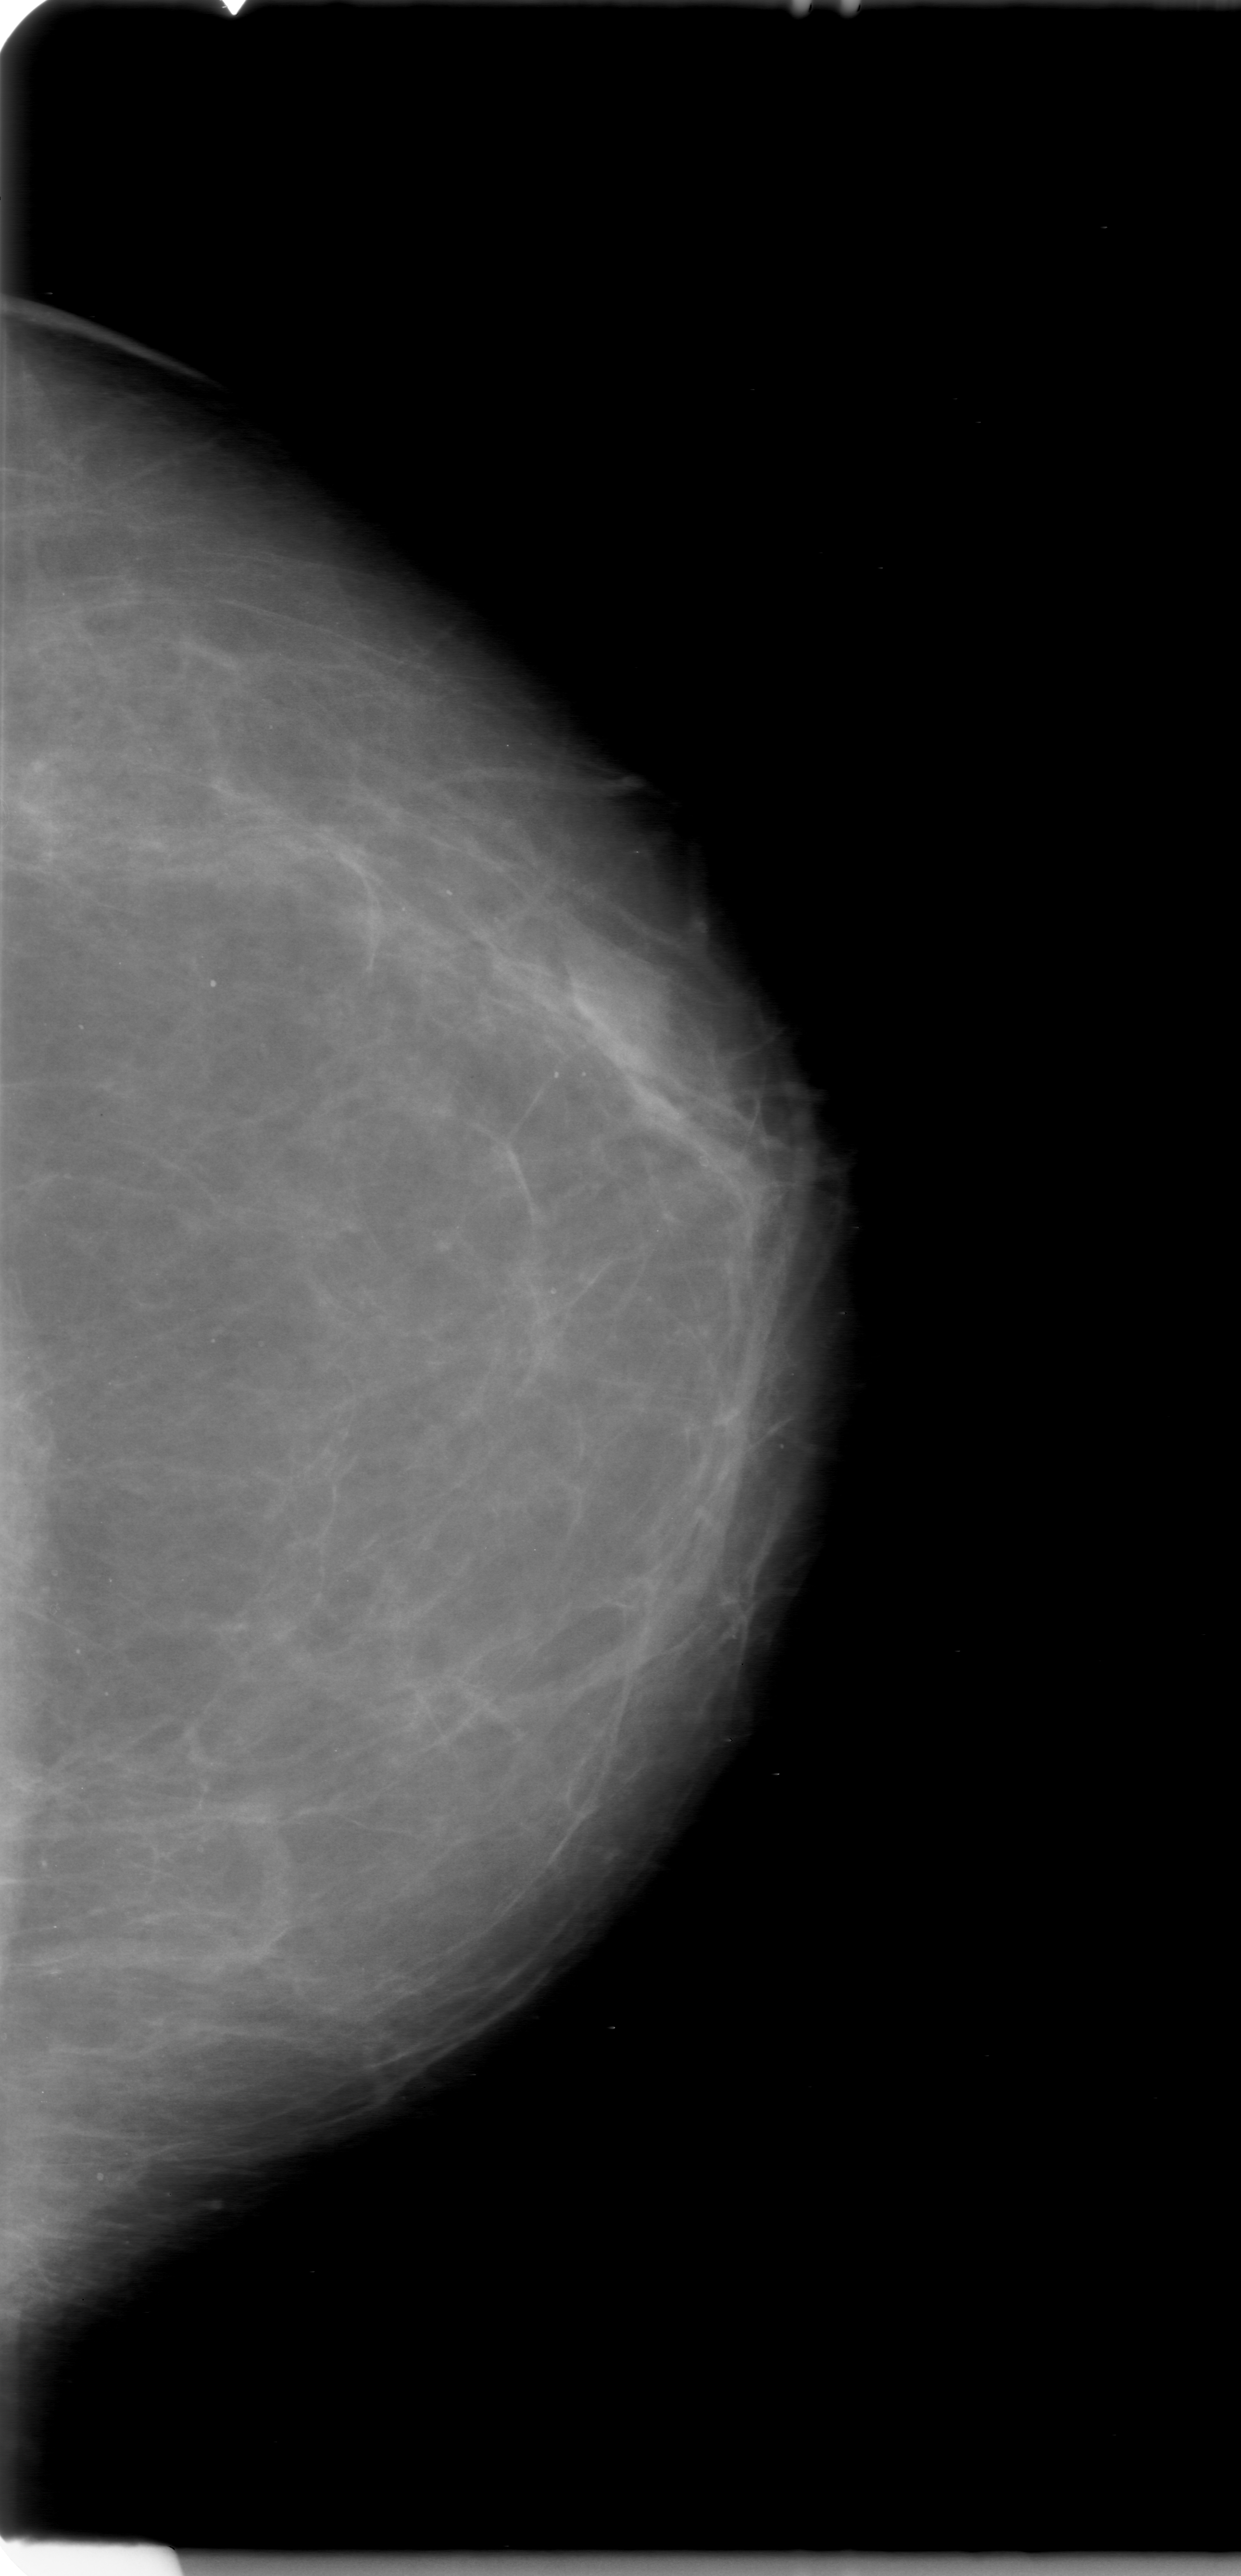
Digitized screen-film mammogram, left breast, craniocaudal (CC) view, BI-RADS breast density category 1 (scale 1–4).
Finding: mass, shape irregular, margins obscured; BI-RADS assessment category 0; subtlety rating 5 on a 1 (subtle) to 5 (obvious) scale; pathology result (as recorded, not read from the image): benign.